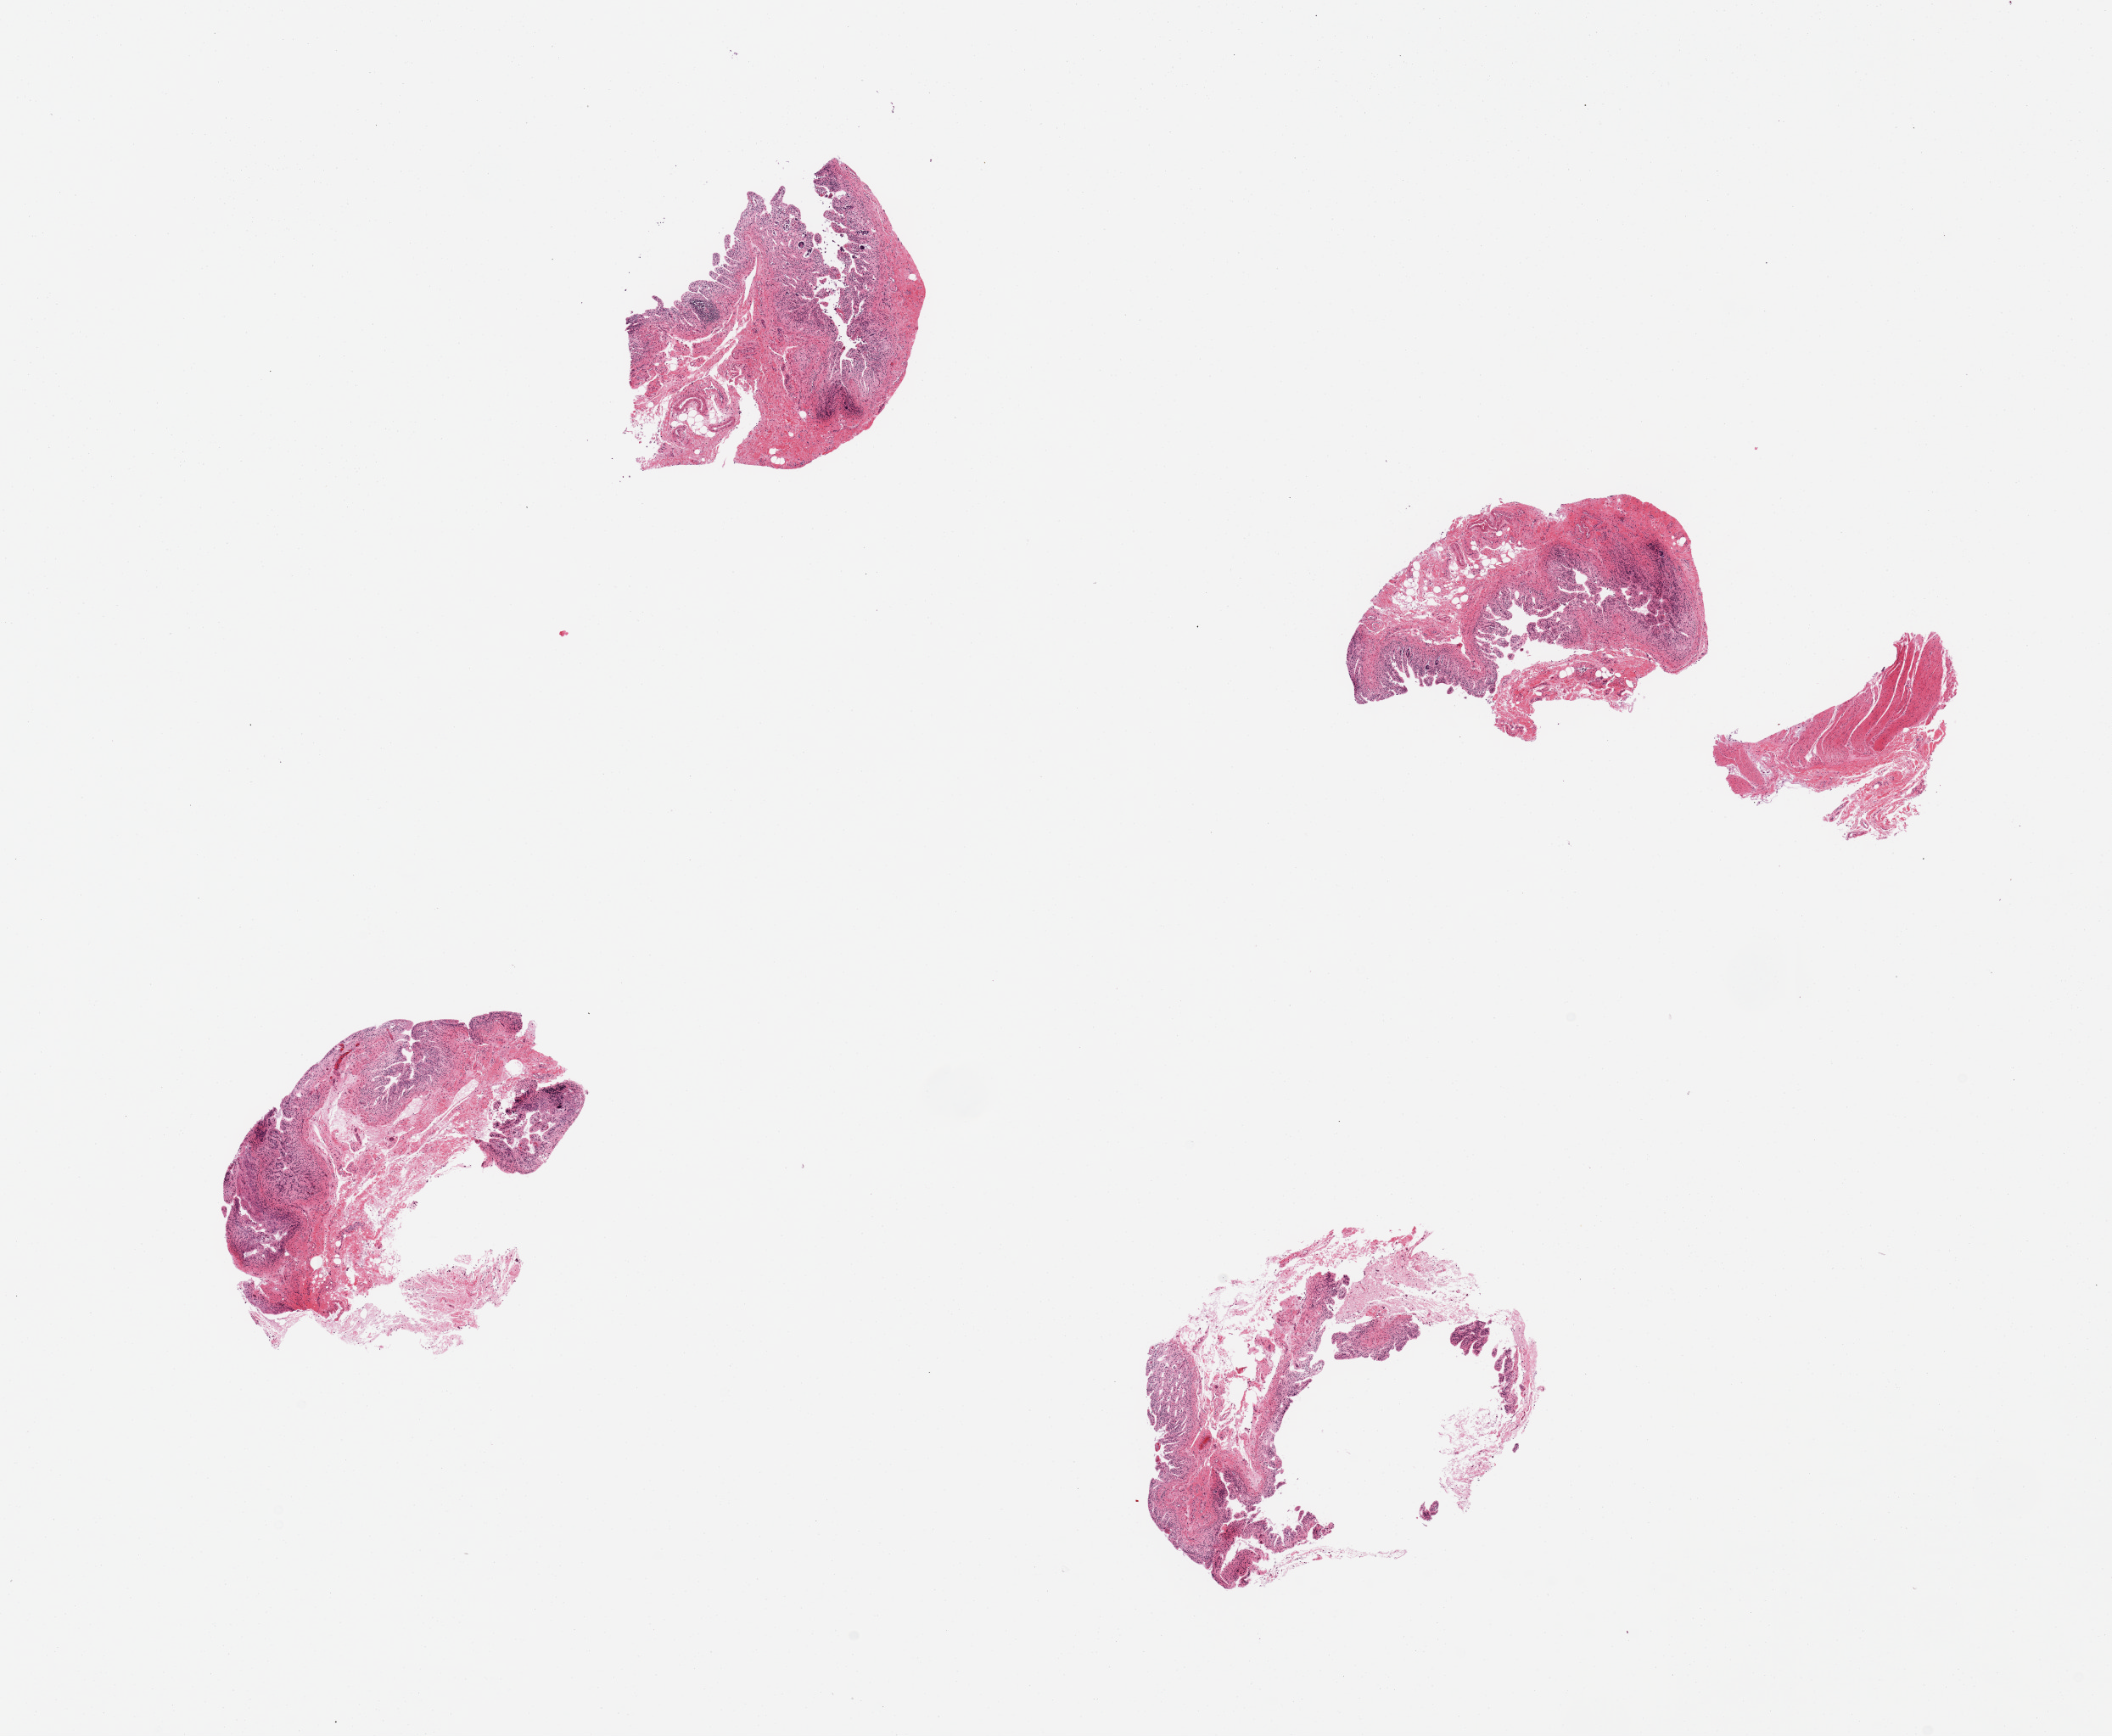
Whole-slide image, hematoxylin and eosin (H&E) stain — whole scanned area (about 19.7 x 16.2 mm, from a 20x scan) shown as a low-resolution overview; PAXgene-fixed paraffin-embedded (PFPE) section; target tissue: ileum; donor tissue sample. Female donor.
* review note (as recorded): 4 pieces, mucosa badly autolyzed; ~10% residual lymphod aggregates present